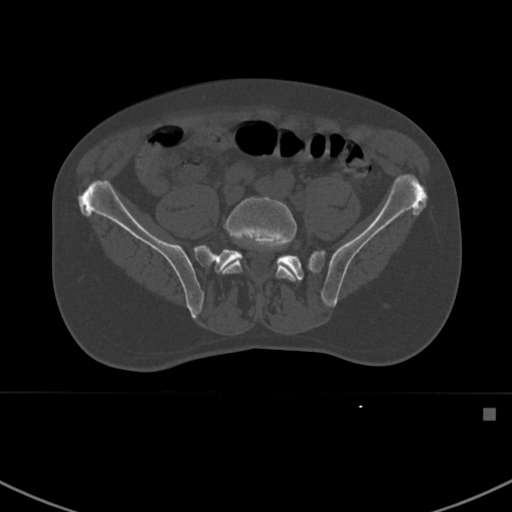
CT including the spine, one axial slice. Position 212 of 412 along the scan axis. Bone window (W 1800 / L 400 HU). 512 × 512 image matrix. Male patient, age 59 years. Case-level facts recorded for this patient, not image findings: primary cancer: prostate.
Structures marked on this image (semi-automatic segmentation, software-assisted and operator-edited):
- L5 vertebra: bounding box <223,196,299,281> (left, top, right, bottom; pixels)